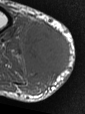
MRI of an extremity soft-tissue mass, one axial slice. Position 18 of 47 along the scan axis. MR volume resampled by the dataset authors to the PET/CT grid (not the native acquisition matrix). 85 × 114 image matrix. Male patient. Case-level facts recorded for this patient, not image findings: histological type: pleiomorphic liposarcoma; grade: high; site of the primary tumour: right calf.
Structures marked on this image (expert contour drawn on MRI and transferred to this co-registered scan by the dataset authors):
- gross tumour volume including surrounding oedema: bounding box <20,19,71,95> (left, top, right, bottom; pixels)
- gross tumour volume (mass): <24,25,71,74>